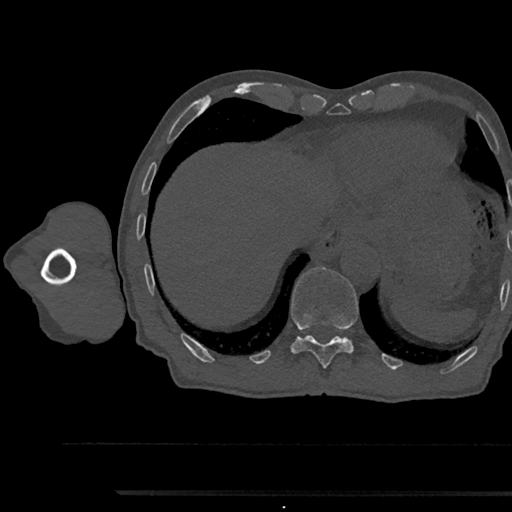
CT including the spine, one axial slice. Position 782 of 797 along the scan axis. 120 kVp. Bone window (W 1800 / L 400 HU). 0.5 mm slice thickness. 512 × 512 image matrix, field of view 367 × 367 mm. Male patient, age 79 years. Case-level facts recorded for this patient, not image findings: primary cancer: prostate.
Structures marked on this image (semi-automatically segmented with operator editing):
- T11 vertebra: bounding box <291,266,359,369> (left, top, right, bottom; pixels)